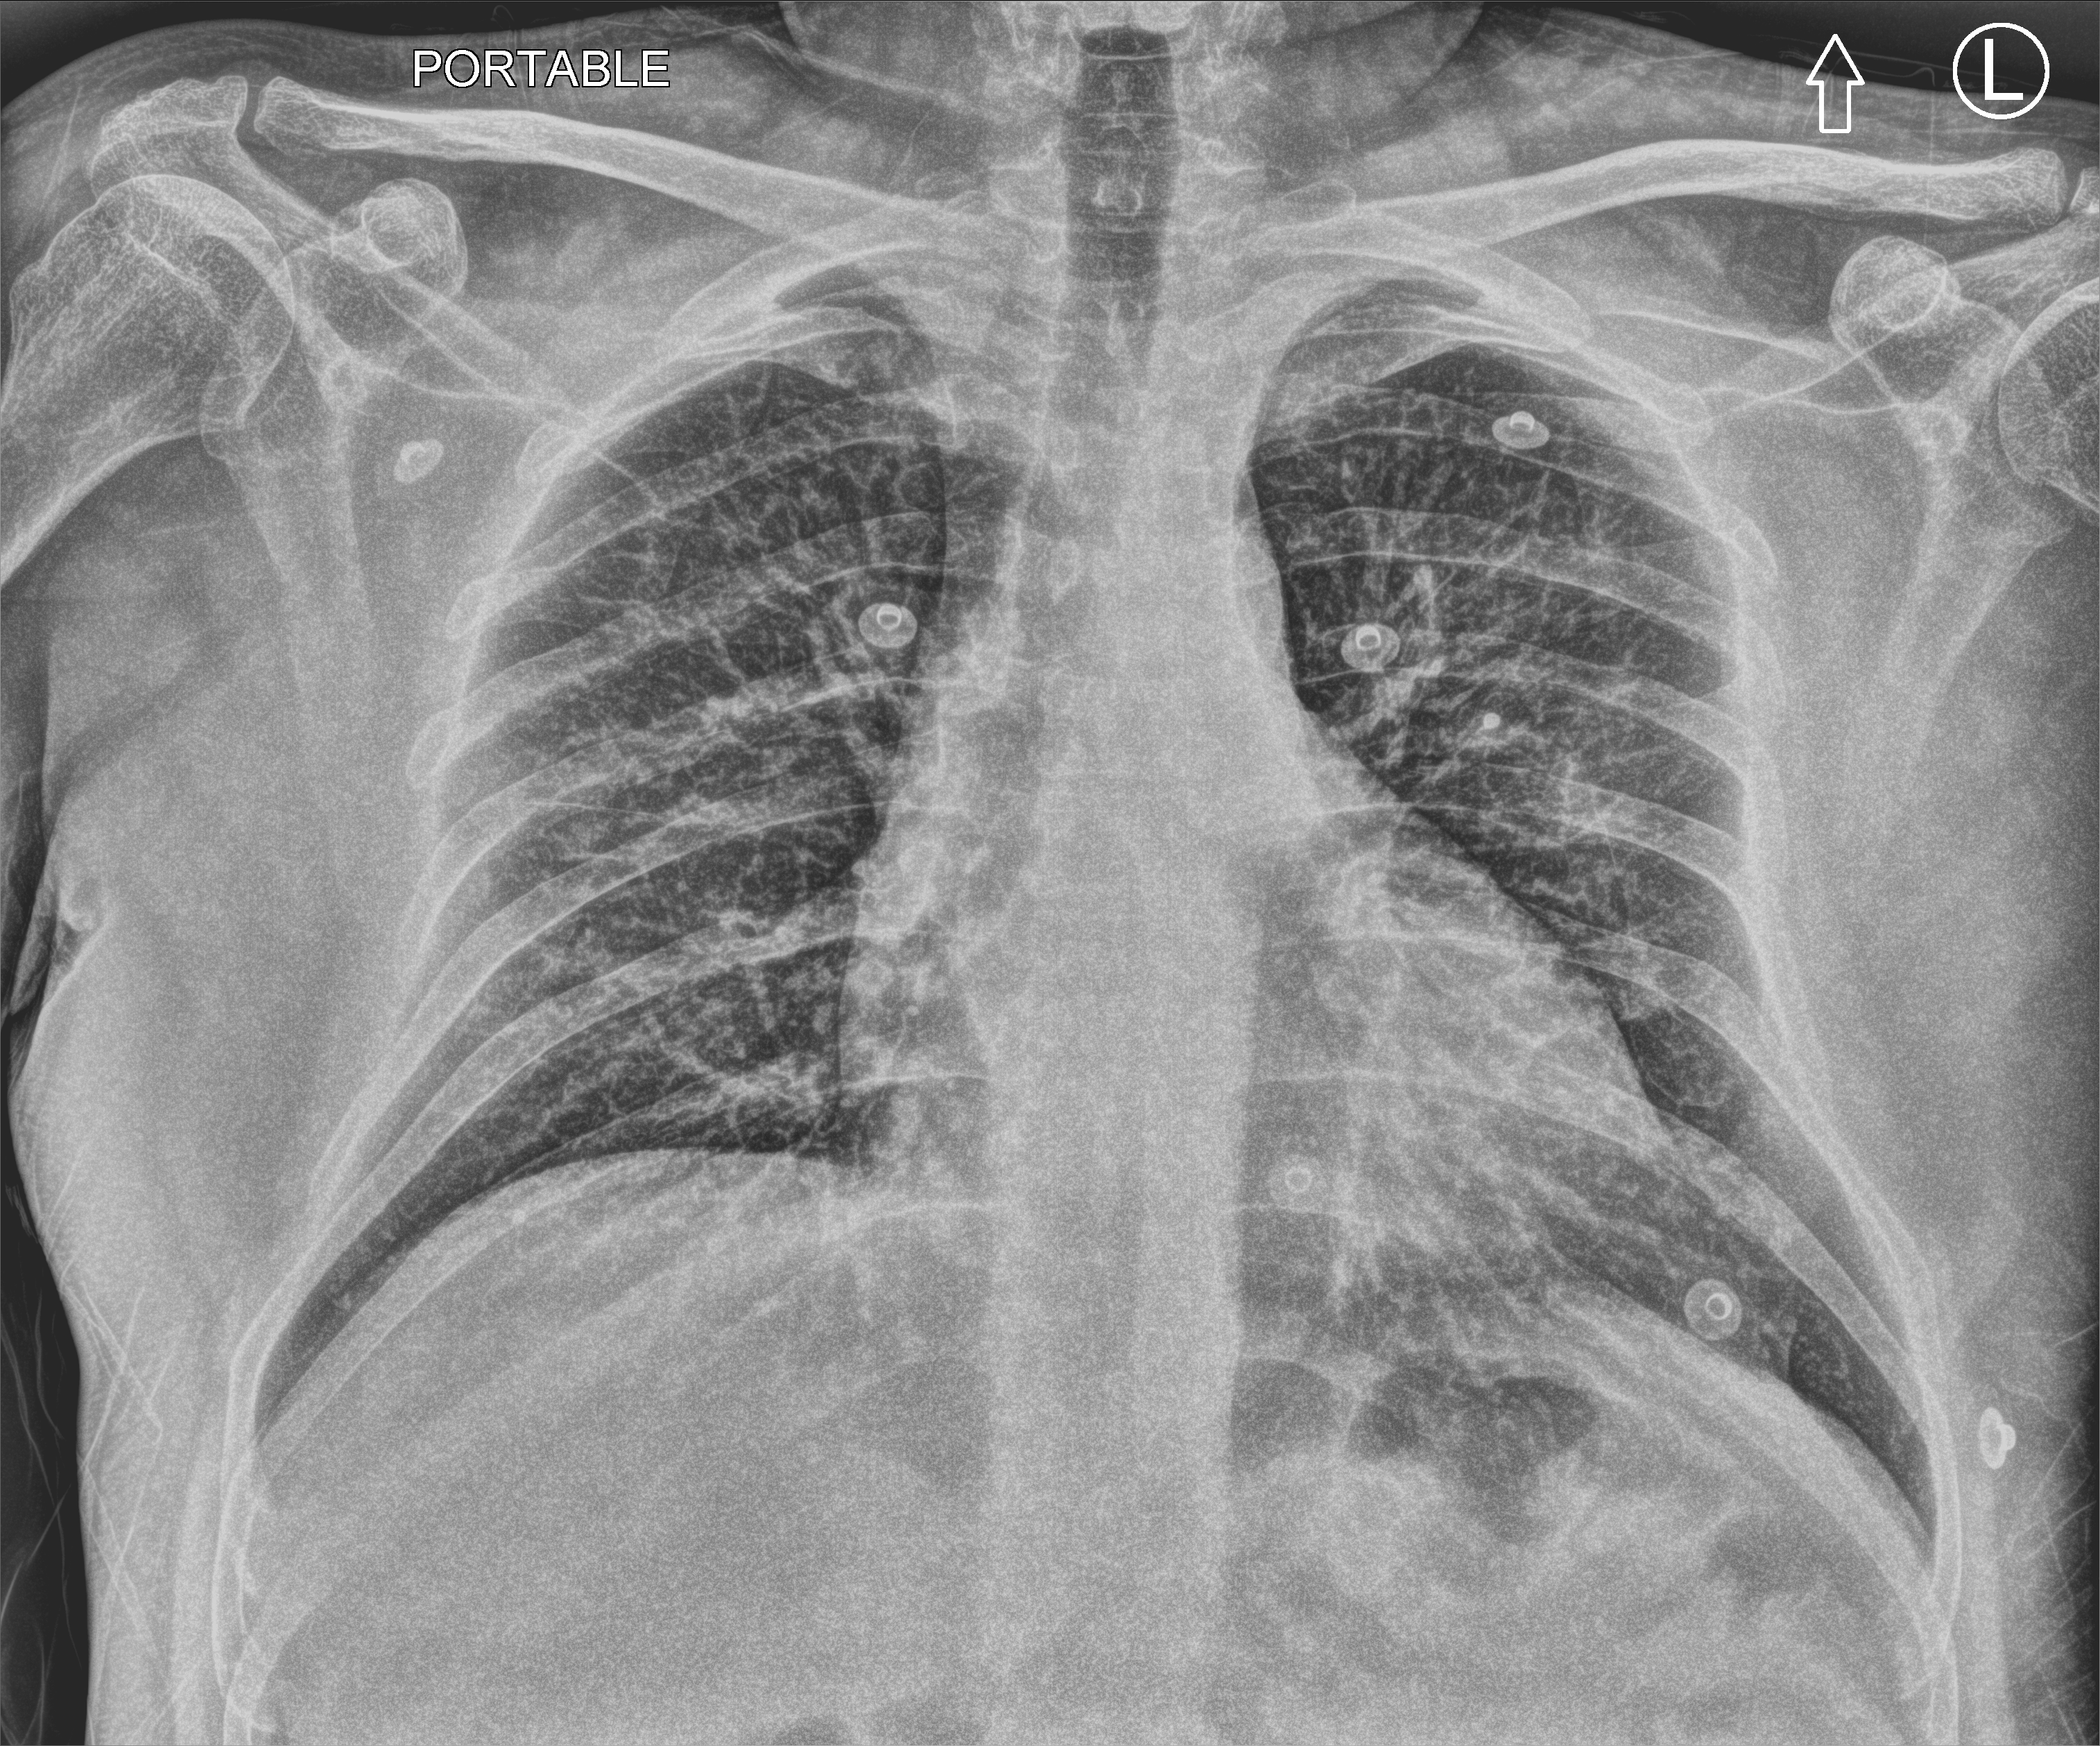
Bedside chest radiograph (computed radiography); anteroposterior (AP) projection. Male patient hospitalised with COVID-19, age 18–59 years.
Admission-level facts for this patient (not findings on this image; timing relative to this image not recorded):
- mechanically ventilated during this hospital stay: no
- admitted to intensive care during this hospital stay: no
- length of hospital stay: 2 days